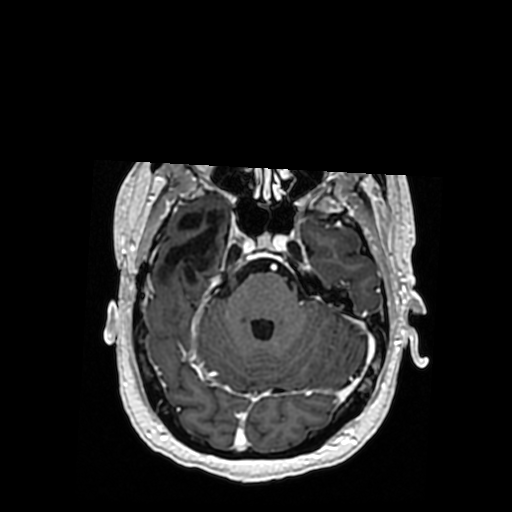
Brain MRI from a brain-tumour surgery series, one axial slice; slice 244 of 364 in the series (ordered by position); T1-weighted post-contrast; 0.5 mm slice thickness; 512 × 512 image matrix, field of view 260 × 260 mm. Case-level facts recorded for this patient, not image findings: histopathology: Oligodendroglioma; WHO grade: 3; IDH mutation: yes; tumour location: Right Posterior Temporal Inferior Parietal.
Annotated regions visible in this slice (outlined manually by an expert reader):
- previous resection cavity: bounding box (x1, y1, x2, y2) in pixels: (160, 210, 227, 278)